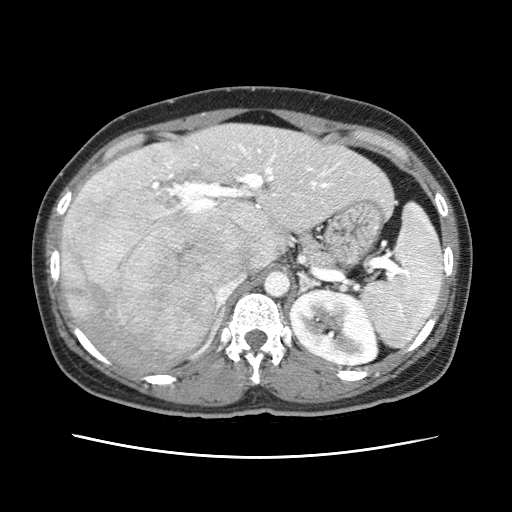
Contrast-enhanced abdominal CT (liver protocol), one axial slice. Position 38 of 79 along the scan axis. Soft-tissue window (W 400 / L 40 HU). 2.5 mm slice thickness. 512 × 512 image matrix, field of view 340 × 340 mm. From the clinical record (not read from this slice): diagnosis: hepatocellular carcinoma (patient treated with transarterial chemoembolisation; whether this scan precedes or follows treatment is not stated here); TNM stage (as recorded): Stage-I; Child-Pugh class: A.
Annotated regions visible in this slice (semi-automatically segmented with operator editing):
- abdominal aorta: box from (x=264, y=271) to (x=289, y=296) px
- liver parenchyma outside the tumour (the mass and vessels are separate outlines, so this box may not span the whole liver): (x=60, y=123)–(x=390, y=370)
- mass: (x=67, y=185)–(x=245, y=366)
- liver vessels: (x=97, y=144)–(x=340, y=212)